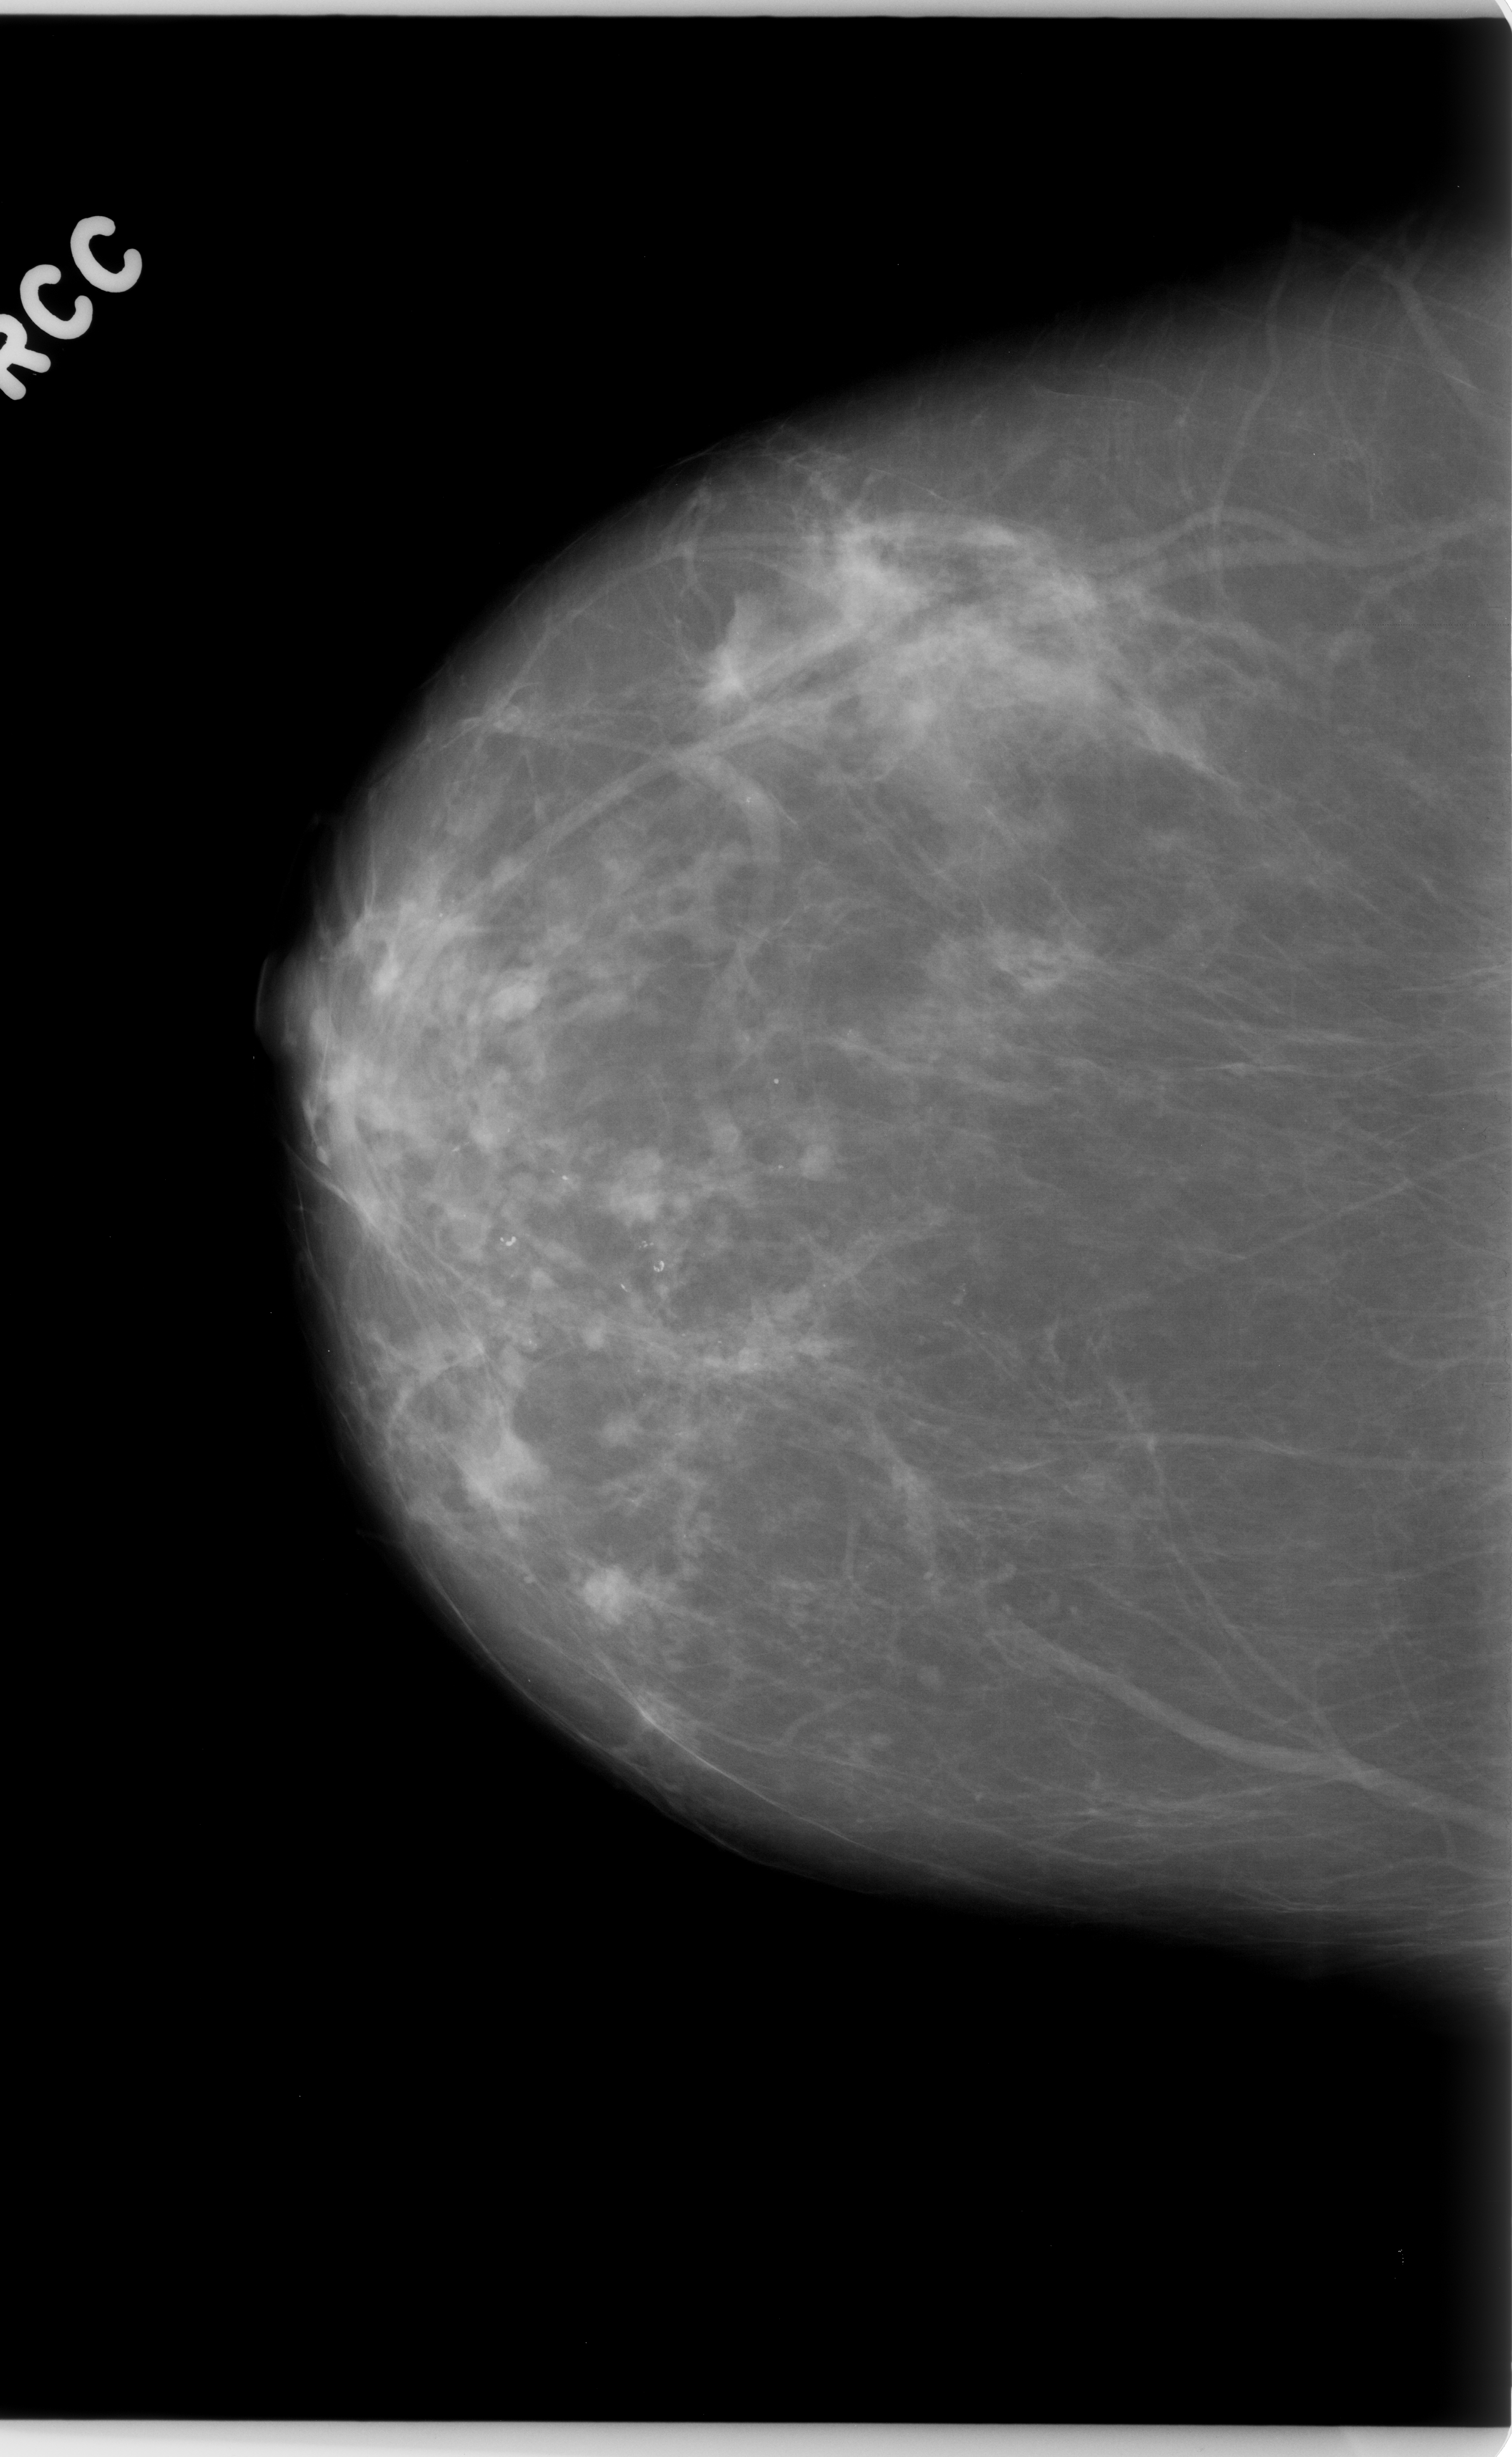
Mammogram (digitized film); right breast; CC view; breast composition: scattered fibroglandular densities (BI-RADS density category 2 of 4).
Calcifications, morphology pleomorphic, distribution segmental; BI-RADS assessment category 4; pathology (as recorded): malignant.